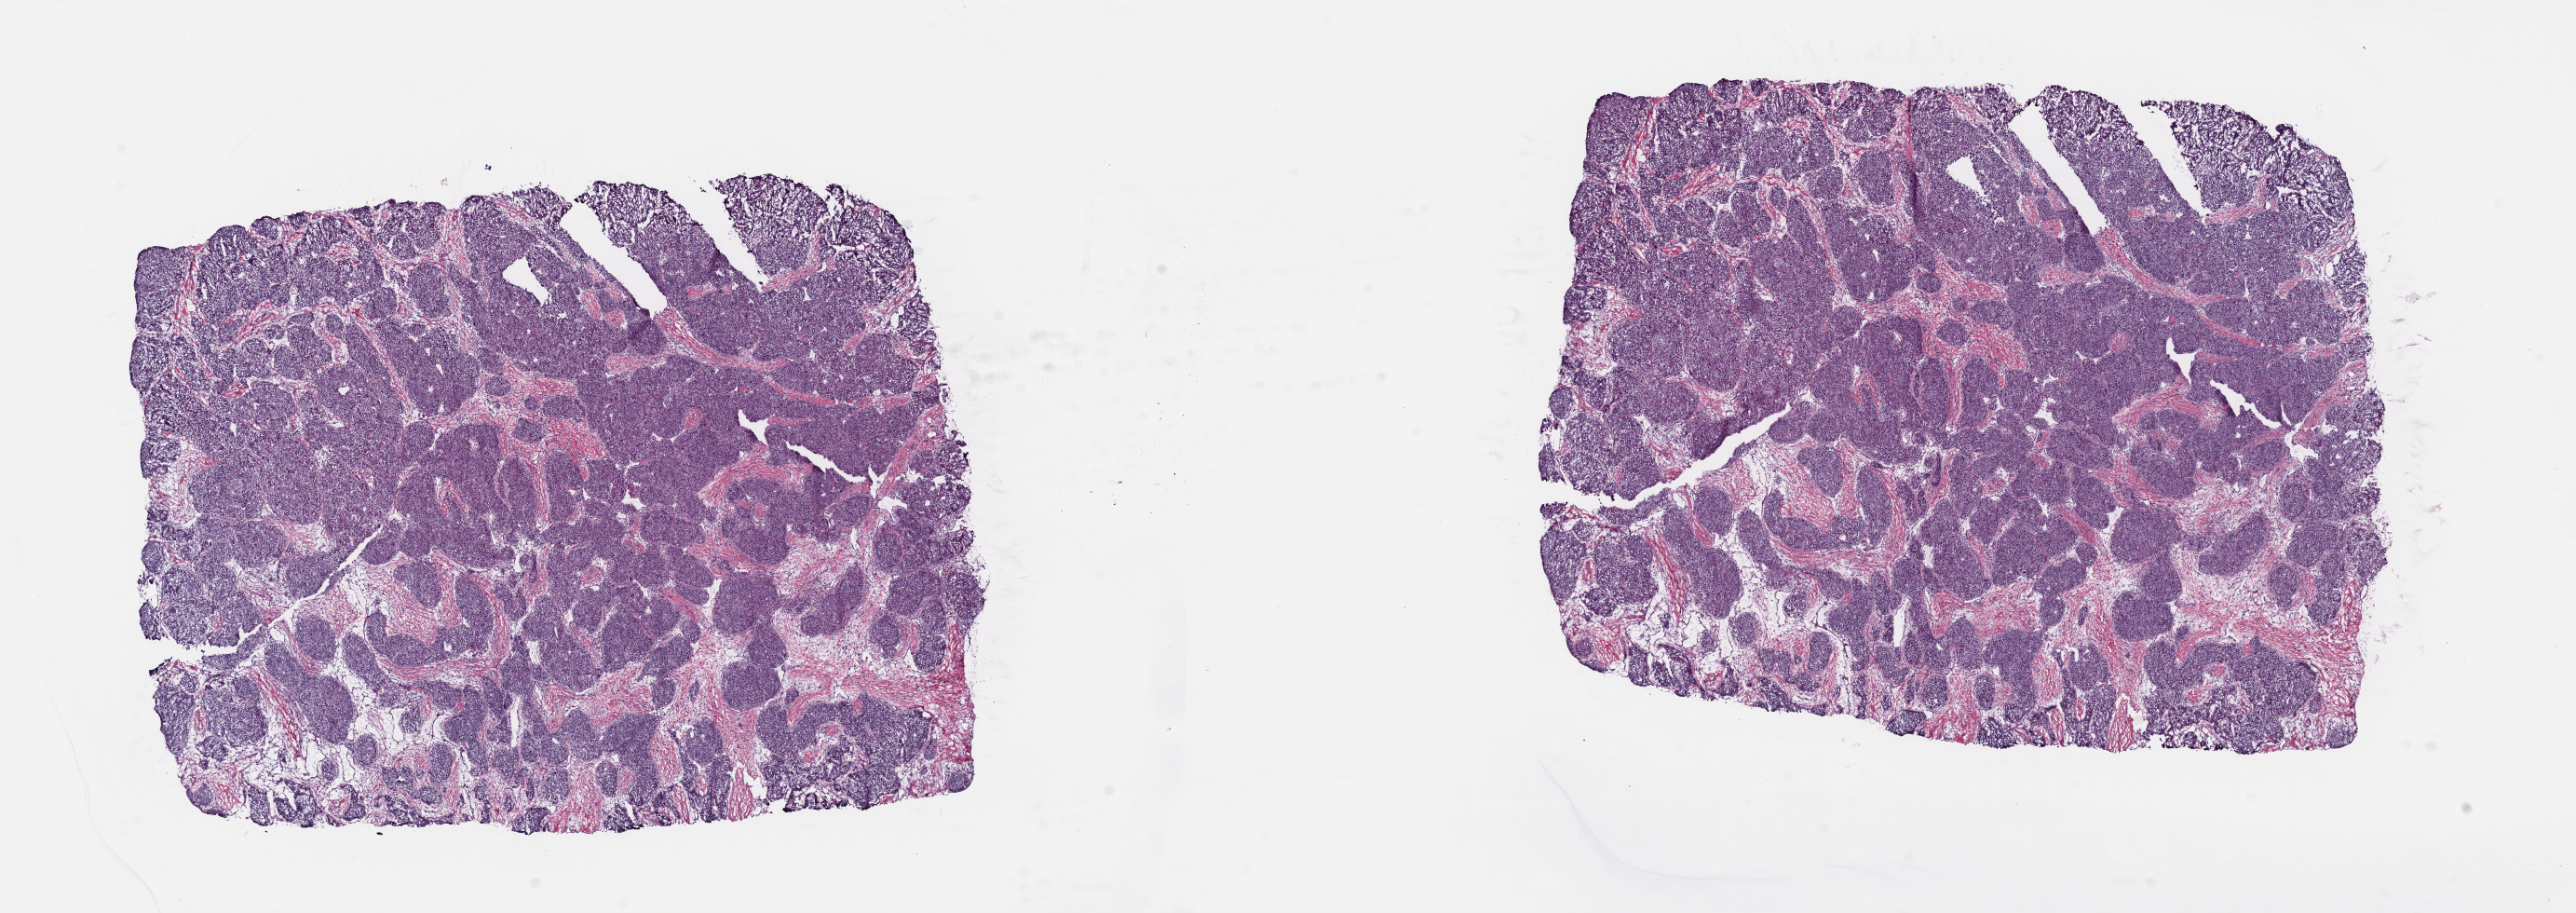
Digitized Hematoxylin and eosin (H&E) stained tissue section (whole slide), a low-resolution overview of the entire scanned area, about 21.8 x 7.7 mm (slide scanned at 40x). Frozen section from the top of the tissue portion. Breast, primary tumour sample. Female, age 53 years at initial diagnosis. Pathologist review of this section (percent, as recorded): tumour cells 100%, tumour nuclei 90%, normal cells 0%, stromal cells 0%, necrosis 0%. Inflammatory infiltration, as recorded: lymphocyte infiltration 0%, monocyte infiltration 0%, neutrophil infiltration 0%.
* lymph nodes positive (case pathology): 0 of 1 examined
* AJCC pathologic stage: IIA
* TNM: T2 N0 M0
* pathologic diagnosis: Infiltrating duct carcinoma, NOS
* laterality: left